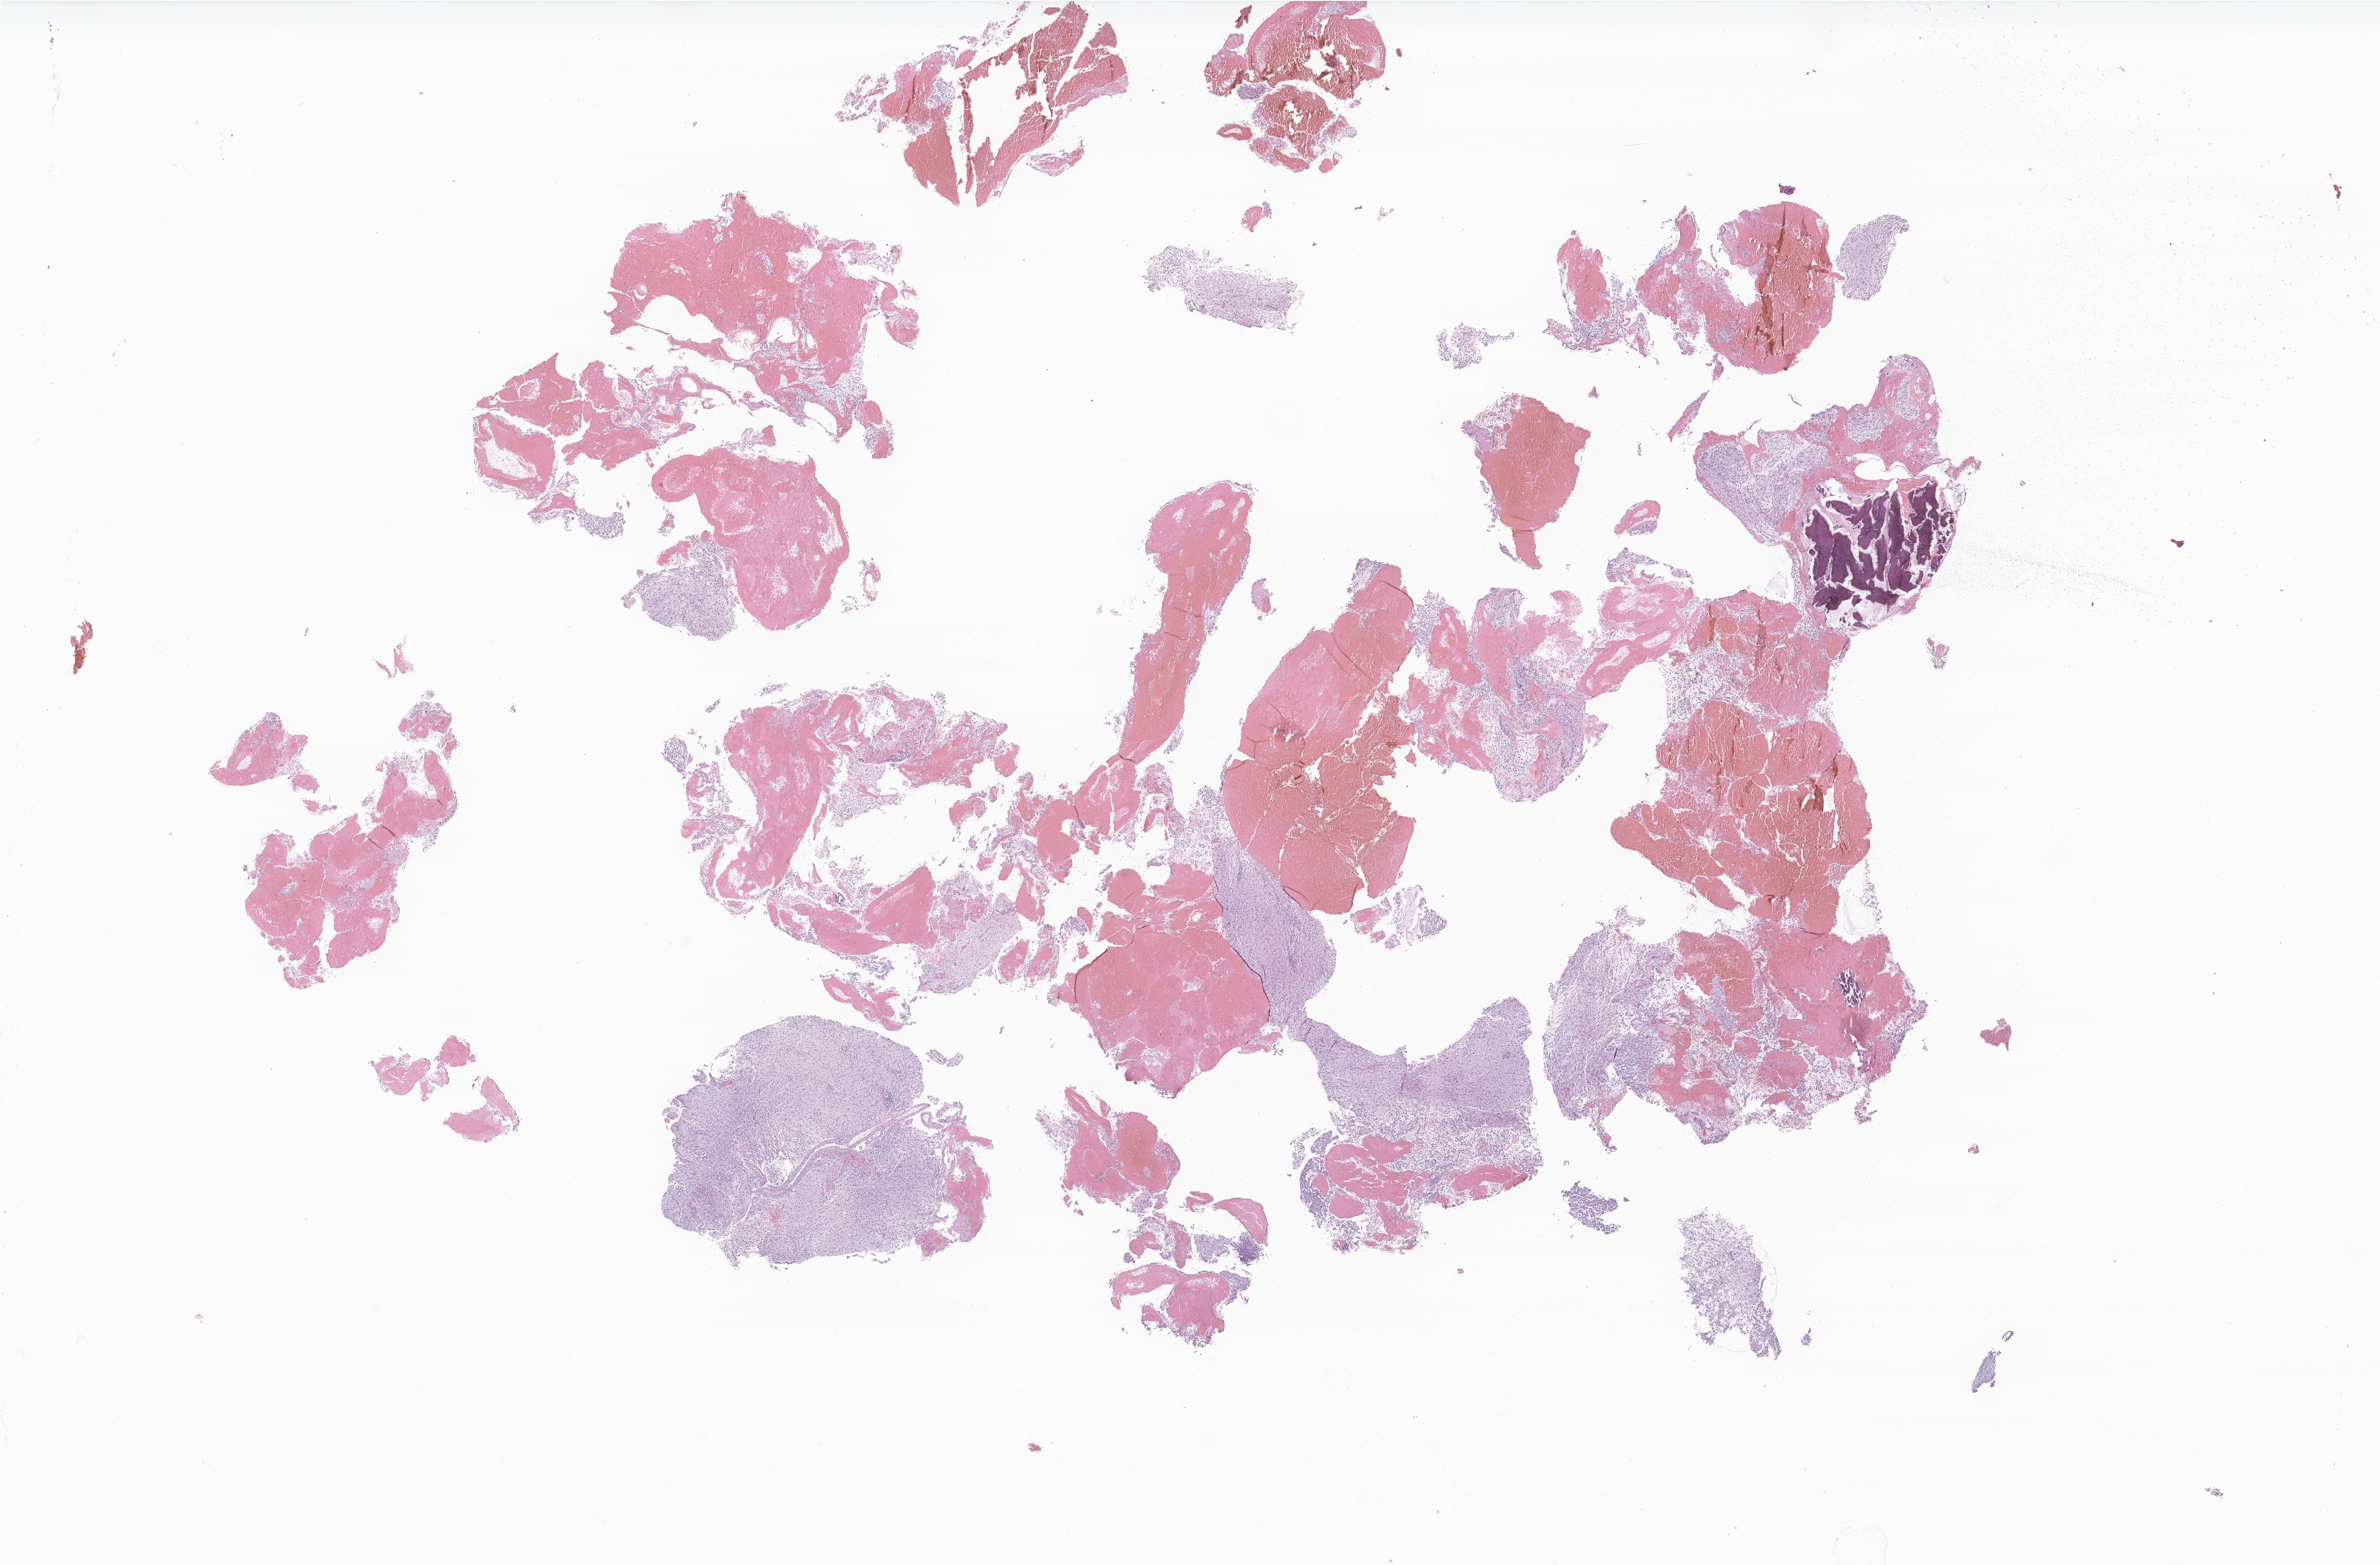
Haematoxylin and eosin whole-slide image of tumor tissue from the optic nerve — whole scanned area (about 21.6 x 14.2 mm) shown as a low-resolution overview, formalin-fixed, paraffin-embedded (FFPE) tissue. Female patient, age 112 months (9 years 4 months).
• diagnosis: Glioma, malignant